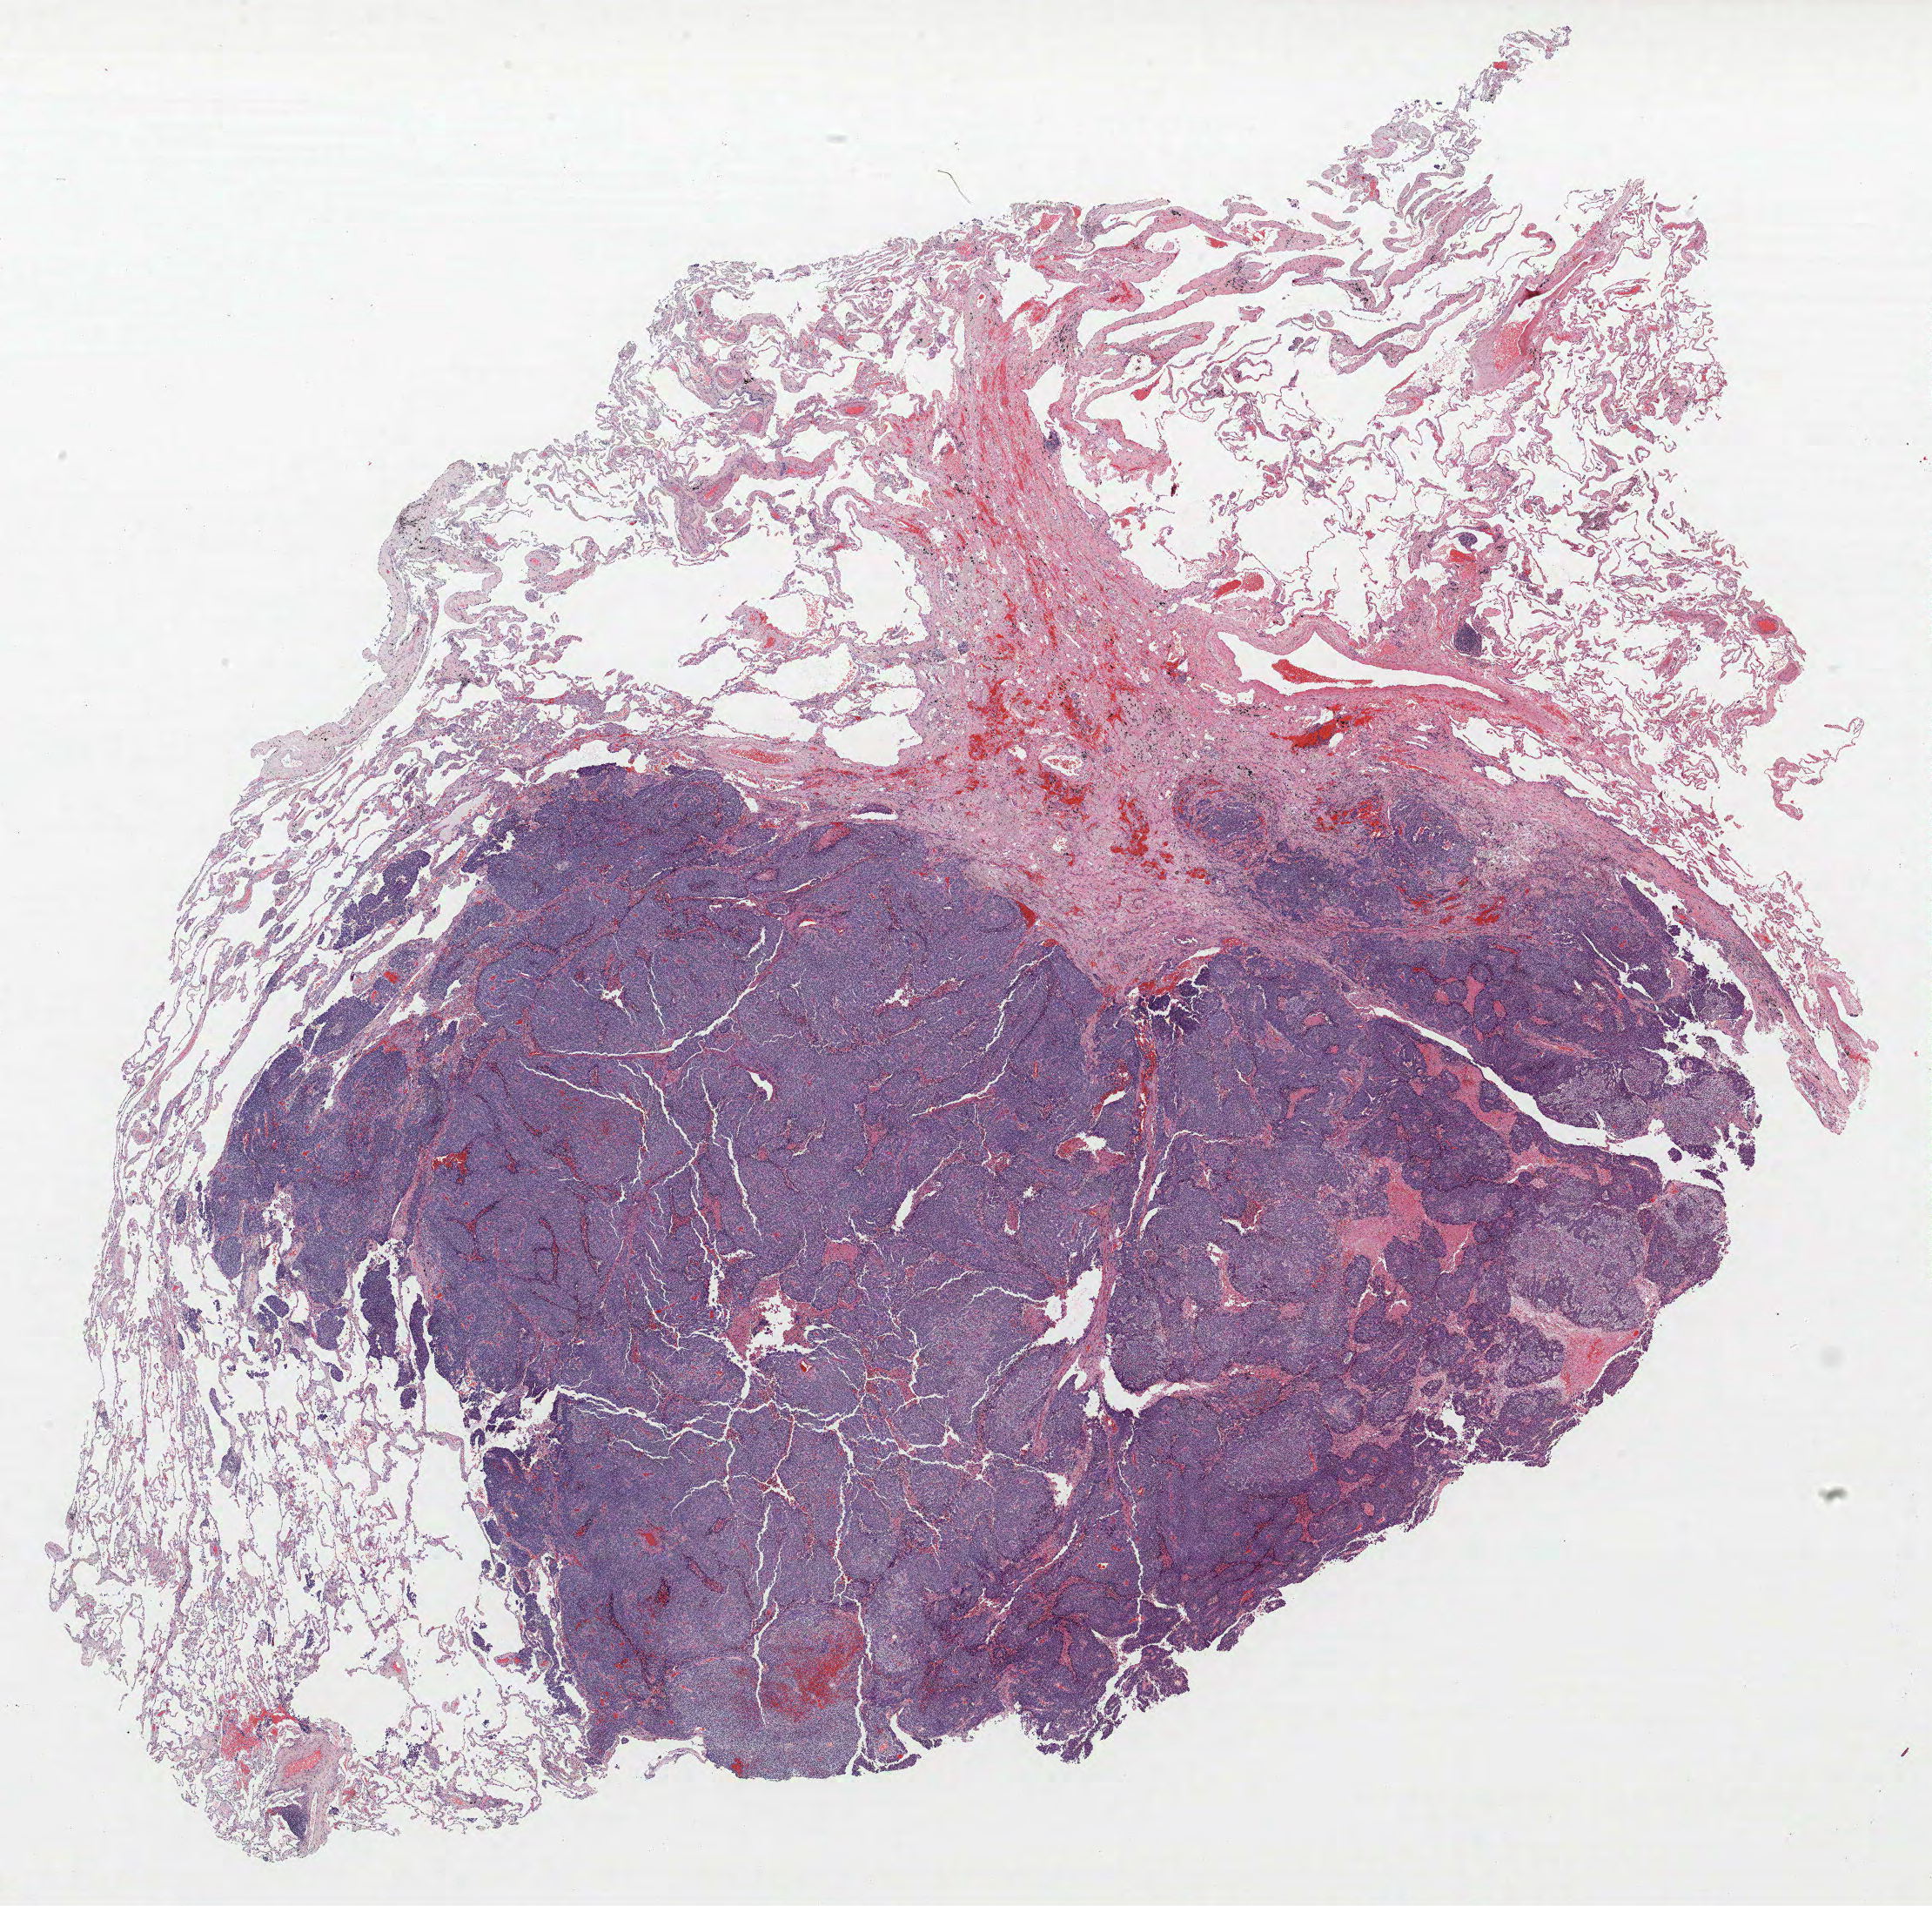
Whole-slide histology image, Hematoxylin and eosin (H&E) stained — a low-resolution overview of the entire scanned area, about 17.8 x 17.5 mm, formalin-fixed paraffin-embedded (FFPE) section, lung. Female, age 70 at enrolment.
Participant's lung-cancer diagnosis: Large cell neuroendocrine carcinoma. Primary tumour location (clinical record): right upper lobe. Stage (AJCC 6th edition): IA. Tumour size (pathology): 30 mm. ICD-O-3 topography: upper lobe of lung (C34.1).